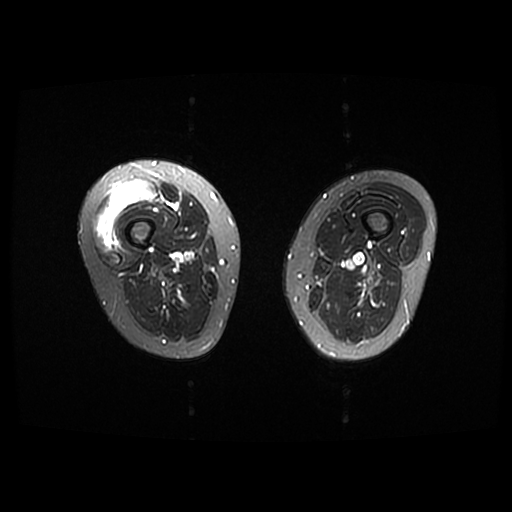
MRI of an extremity soft-tissue mass, one axial slice; position 6 of 42 along the scan axis; T2-weighted fat-saturated; 512 × 512 image matrix, field of view 440 × 440 mm. Female patient. From the clinical record (not read from this slice): histological type: pleiomorphic undifferentiated sarcoma; grade: high; site of the primary tumour: right quadricep.
Outlined on this slice (expert manual segmentation):
- gross tumour volume including surrounding oedema: bounding box (x1, y1, x2, y2) in pixels: (94, 180, 157, 251)